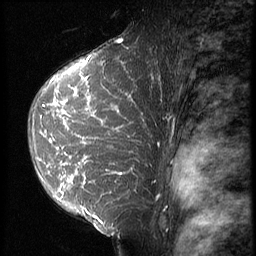
Breast MRI (dynamic contrast-enhanced), one sagittal slice; position 41 of 64 along the scan axis; 3 images stored at this slice position (order not interpretable as contrast timing); 1.5 T; TE 4.2 ms, TR 9 ms; 2.5 mm slice thickness; 256 × 256 image matrix. Patient: female, 39 years. From the clinical record (not read from this slice): setting: breast cancer imaged before/during neoadjuvant chemotherapy; receptor status: HER2-positive.
Outlined on this slice (semi-automatically segmented with operator editing):
- analysis volume of interest (the breast-tissue region the enhancement analysis was run in; not a lesion): bounding box [x1, y1, x2, y2] px = [27, 47, 155, 239]
- tumour enhancement mask (voxels above the 140 % enhancement threshold inside the analysis volume of interest): [39, 62, 133, 218]